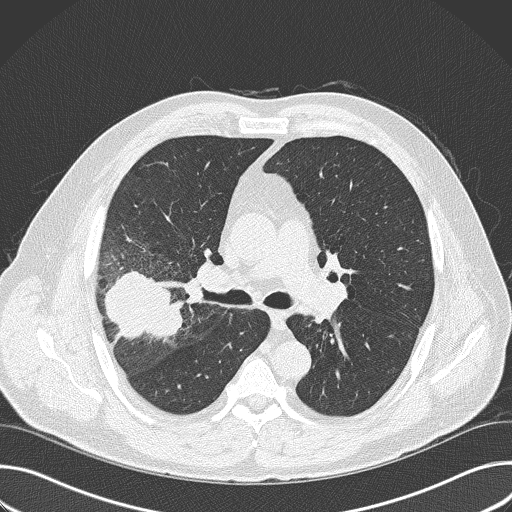
Low-dose screening chest CT, axial slice, baseline screening round, lung window (W 1500 / L -600 HU), lung (sharp) reconstruction kernel (B50f). Male, age 56 years at enrolment. Current smoker at enrolment.
• Expert-annotated lung lesion, bounding box (x1, y1, x2, y2) in pixels: (81, 260, 185, 365).
• Screening reader's record for this exam (one nodule recorded; not confirmed to be the boxed lesion): non-calcified nodule or mass ≥4 mm, right upper lobe, 6 × 5 mm, spiculated (stellate) margins, soft tissue attenuation.